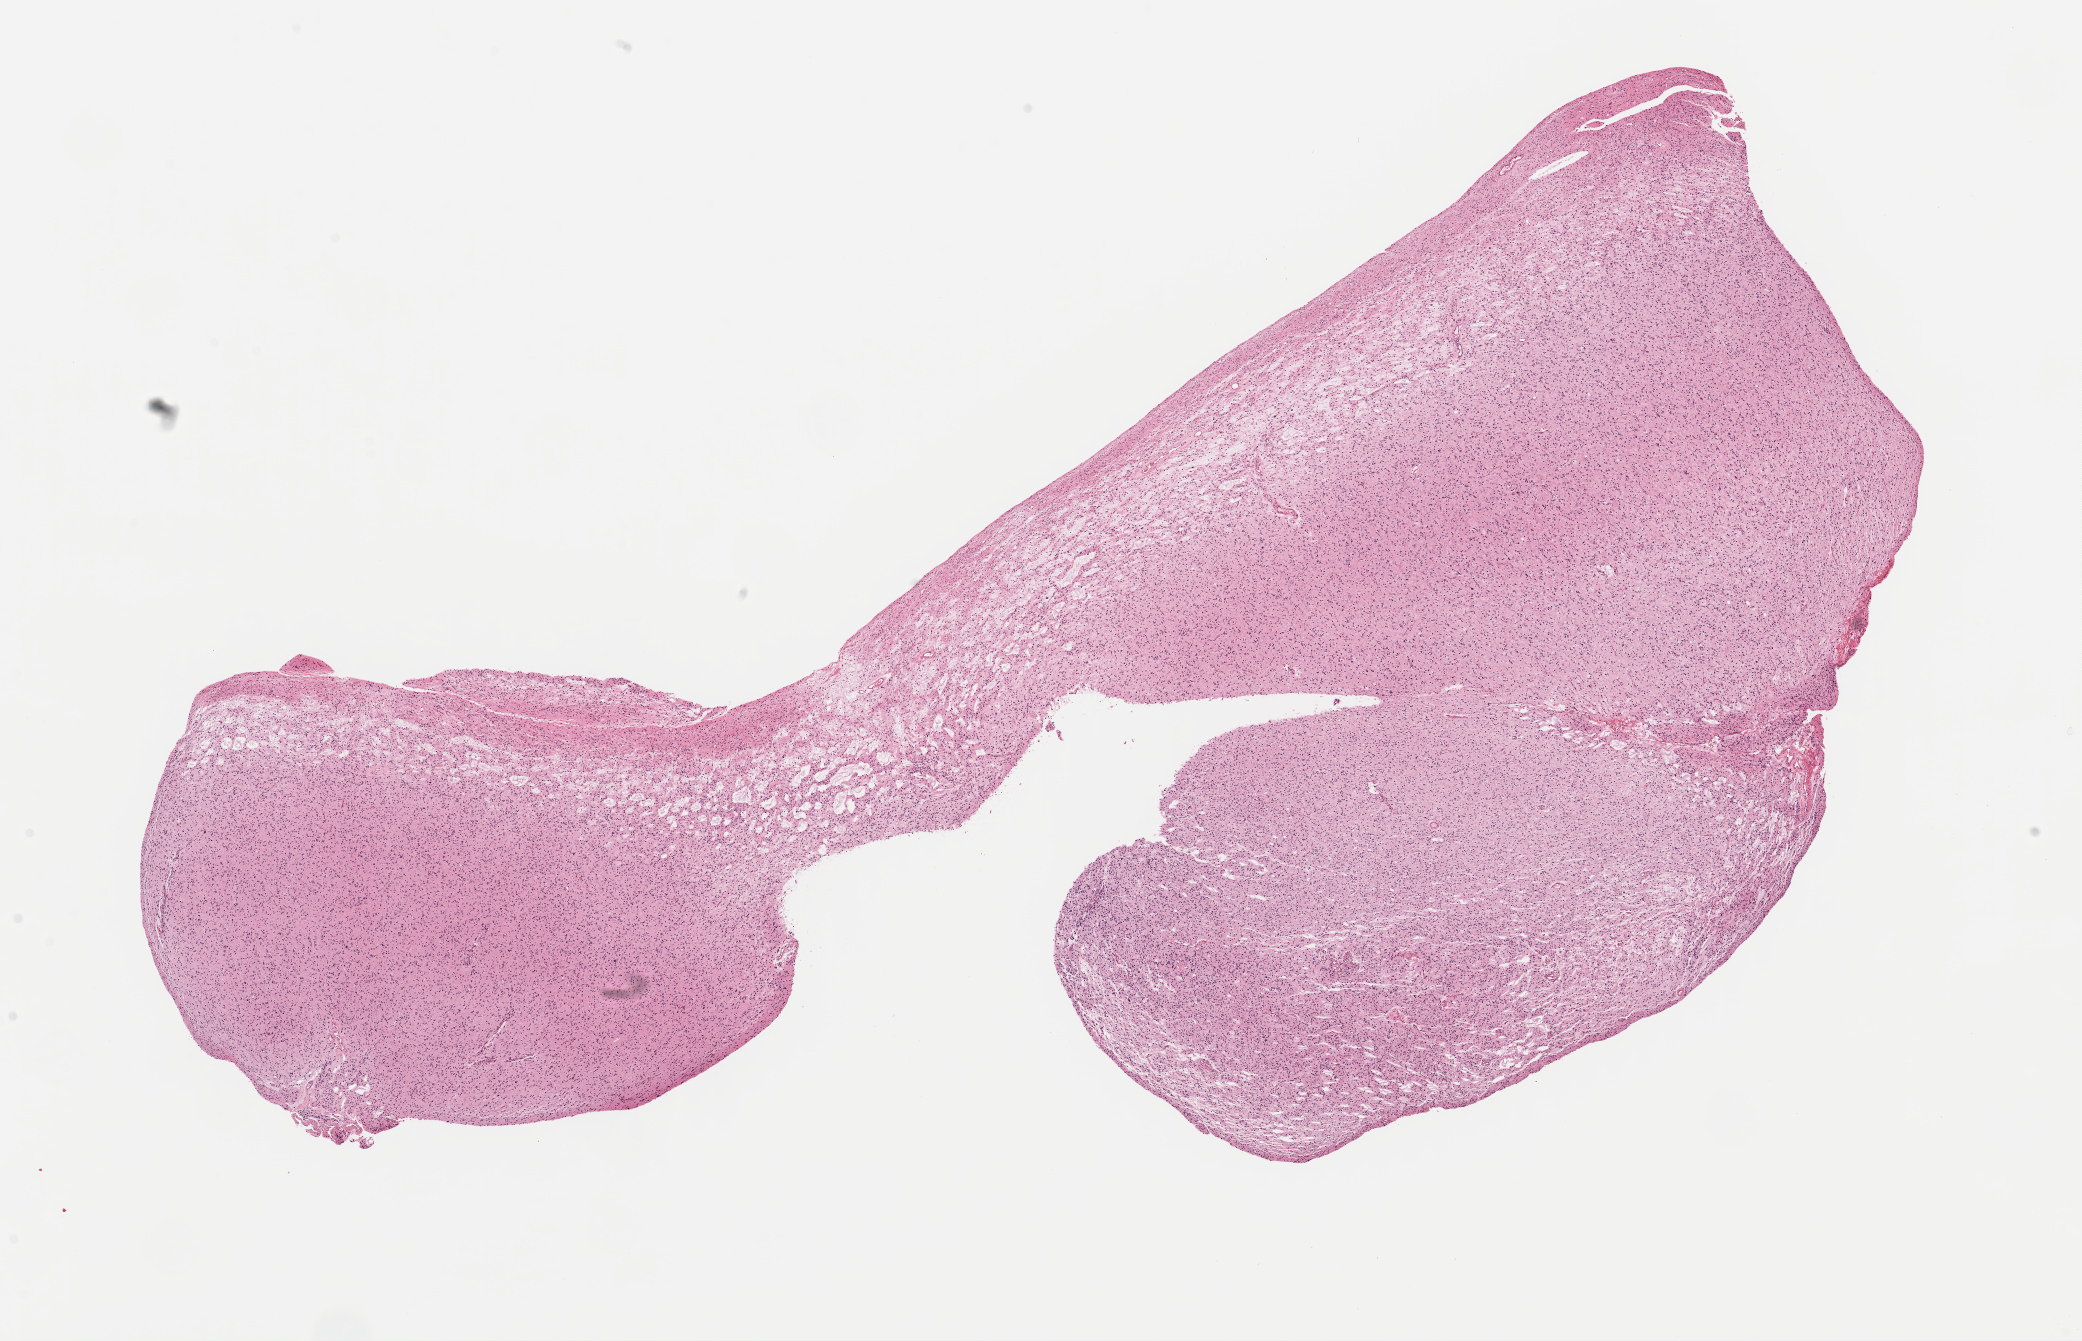
Digitized H&E-stained tissue section (whole slide) — low-resolution overview of the scanned area, about 16.4 x 10.6 mm. Formalin-fixed paraffin-embedded (FFPE) diagnostic section. Brain, primary tumour sample. Female, age 44 years at initial diagnosis. Histologic grade: G2 (moderately differentiated).
Pathologic diagnosis: Mixed glioma (parietal lobe).